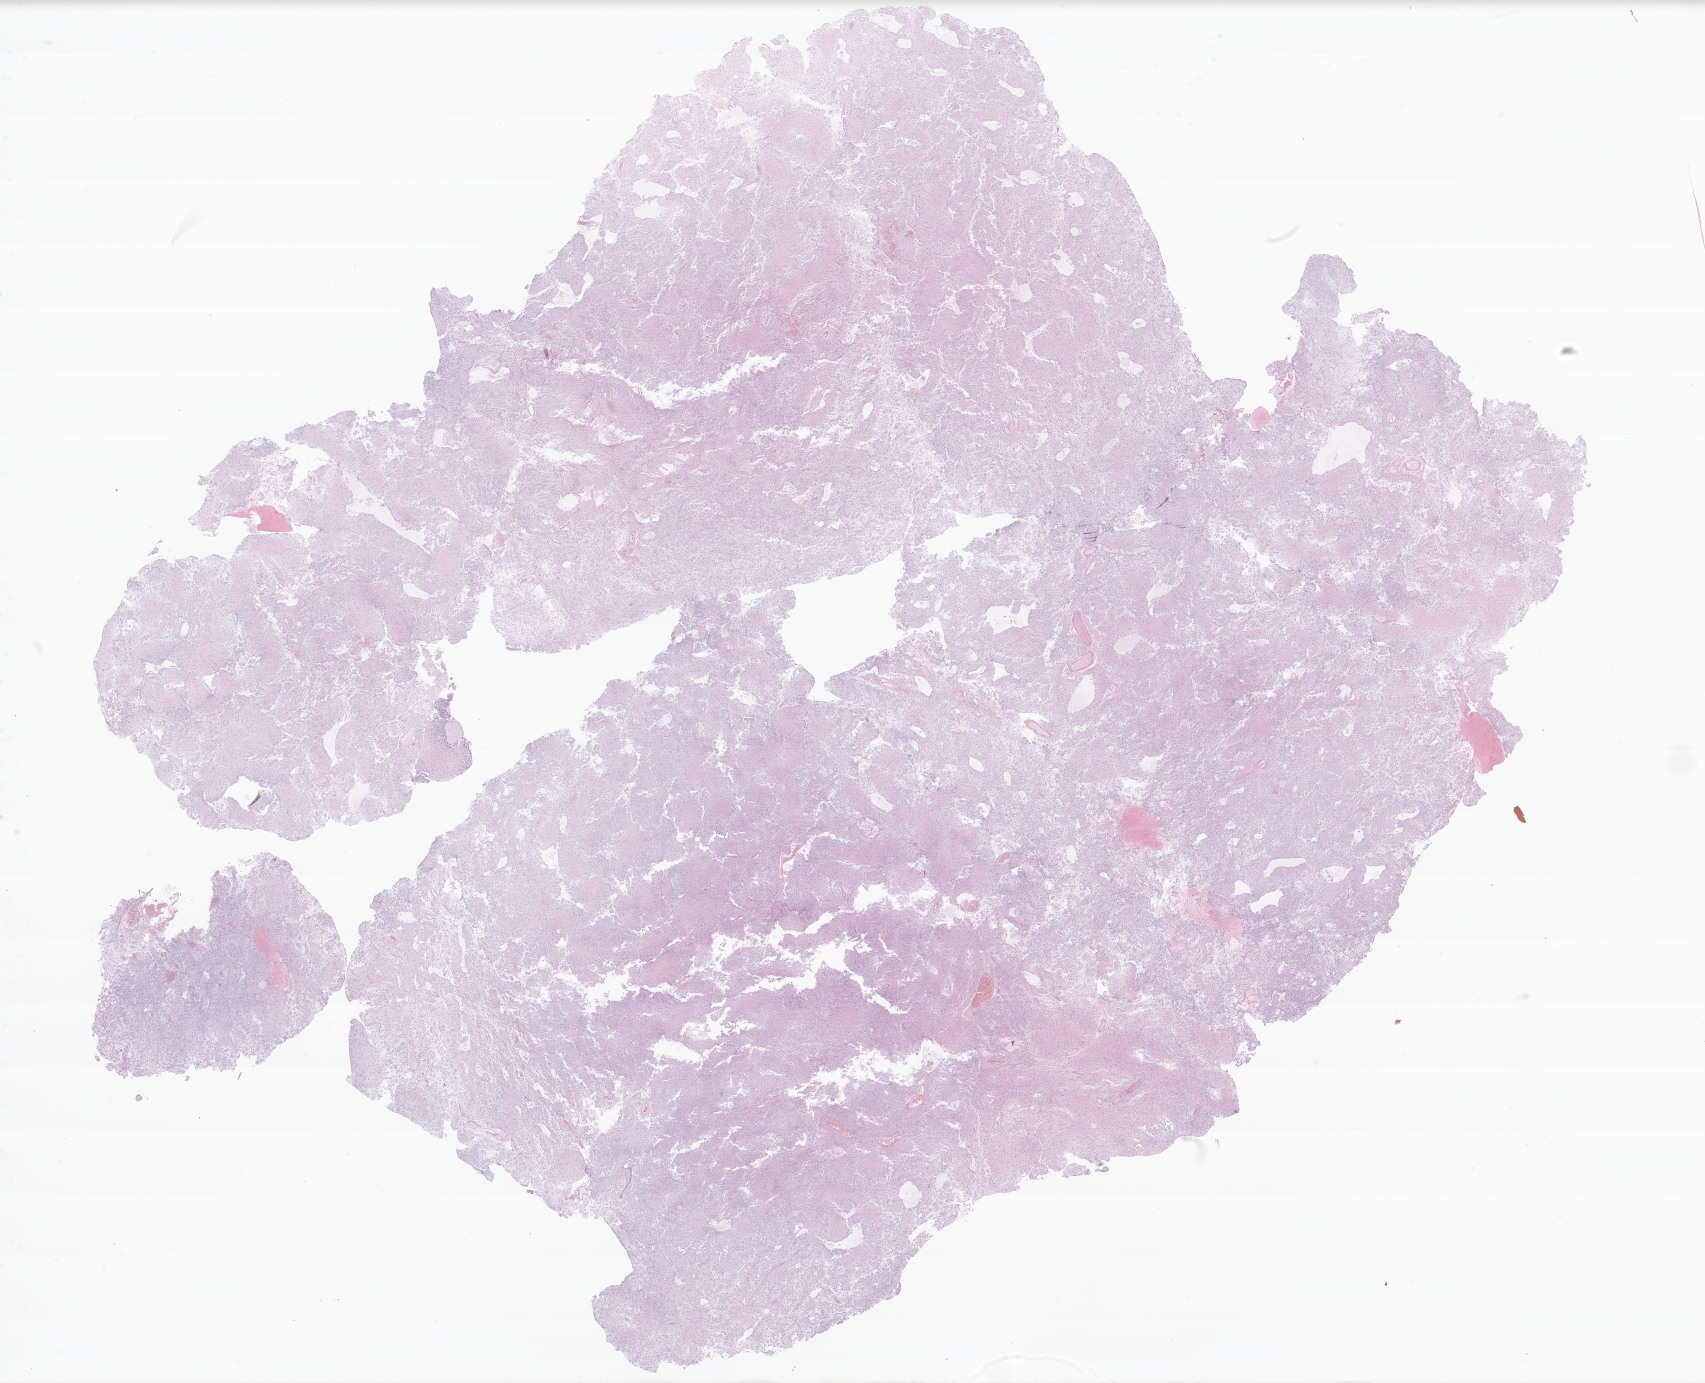
Haematoxylin and eosin whole-slide image of tumor tissue from the brain, a low-resolution overview of the entire scanned area, about 28.7 x 23.3 mm, formalin-fixed, paraffin-embedded (FFPE) tissue. Patient female; age 82 months.
Diagnosis (ICD-O-3 morphology term): Pilocytic astrocytoma.